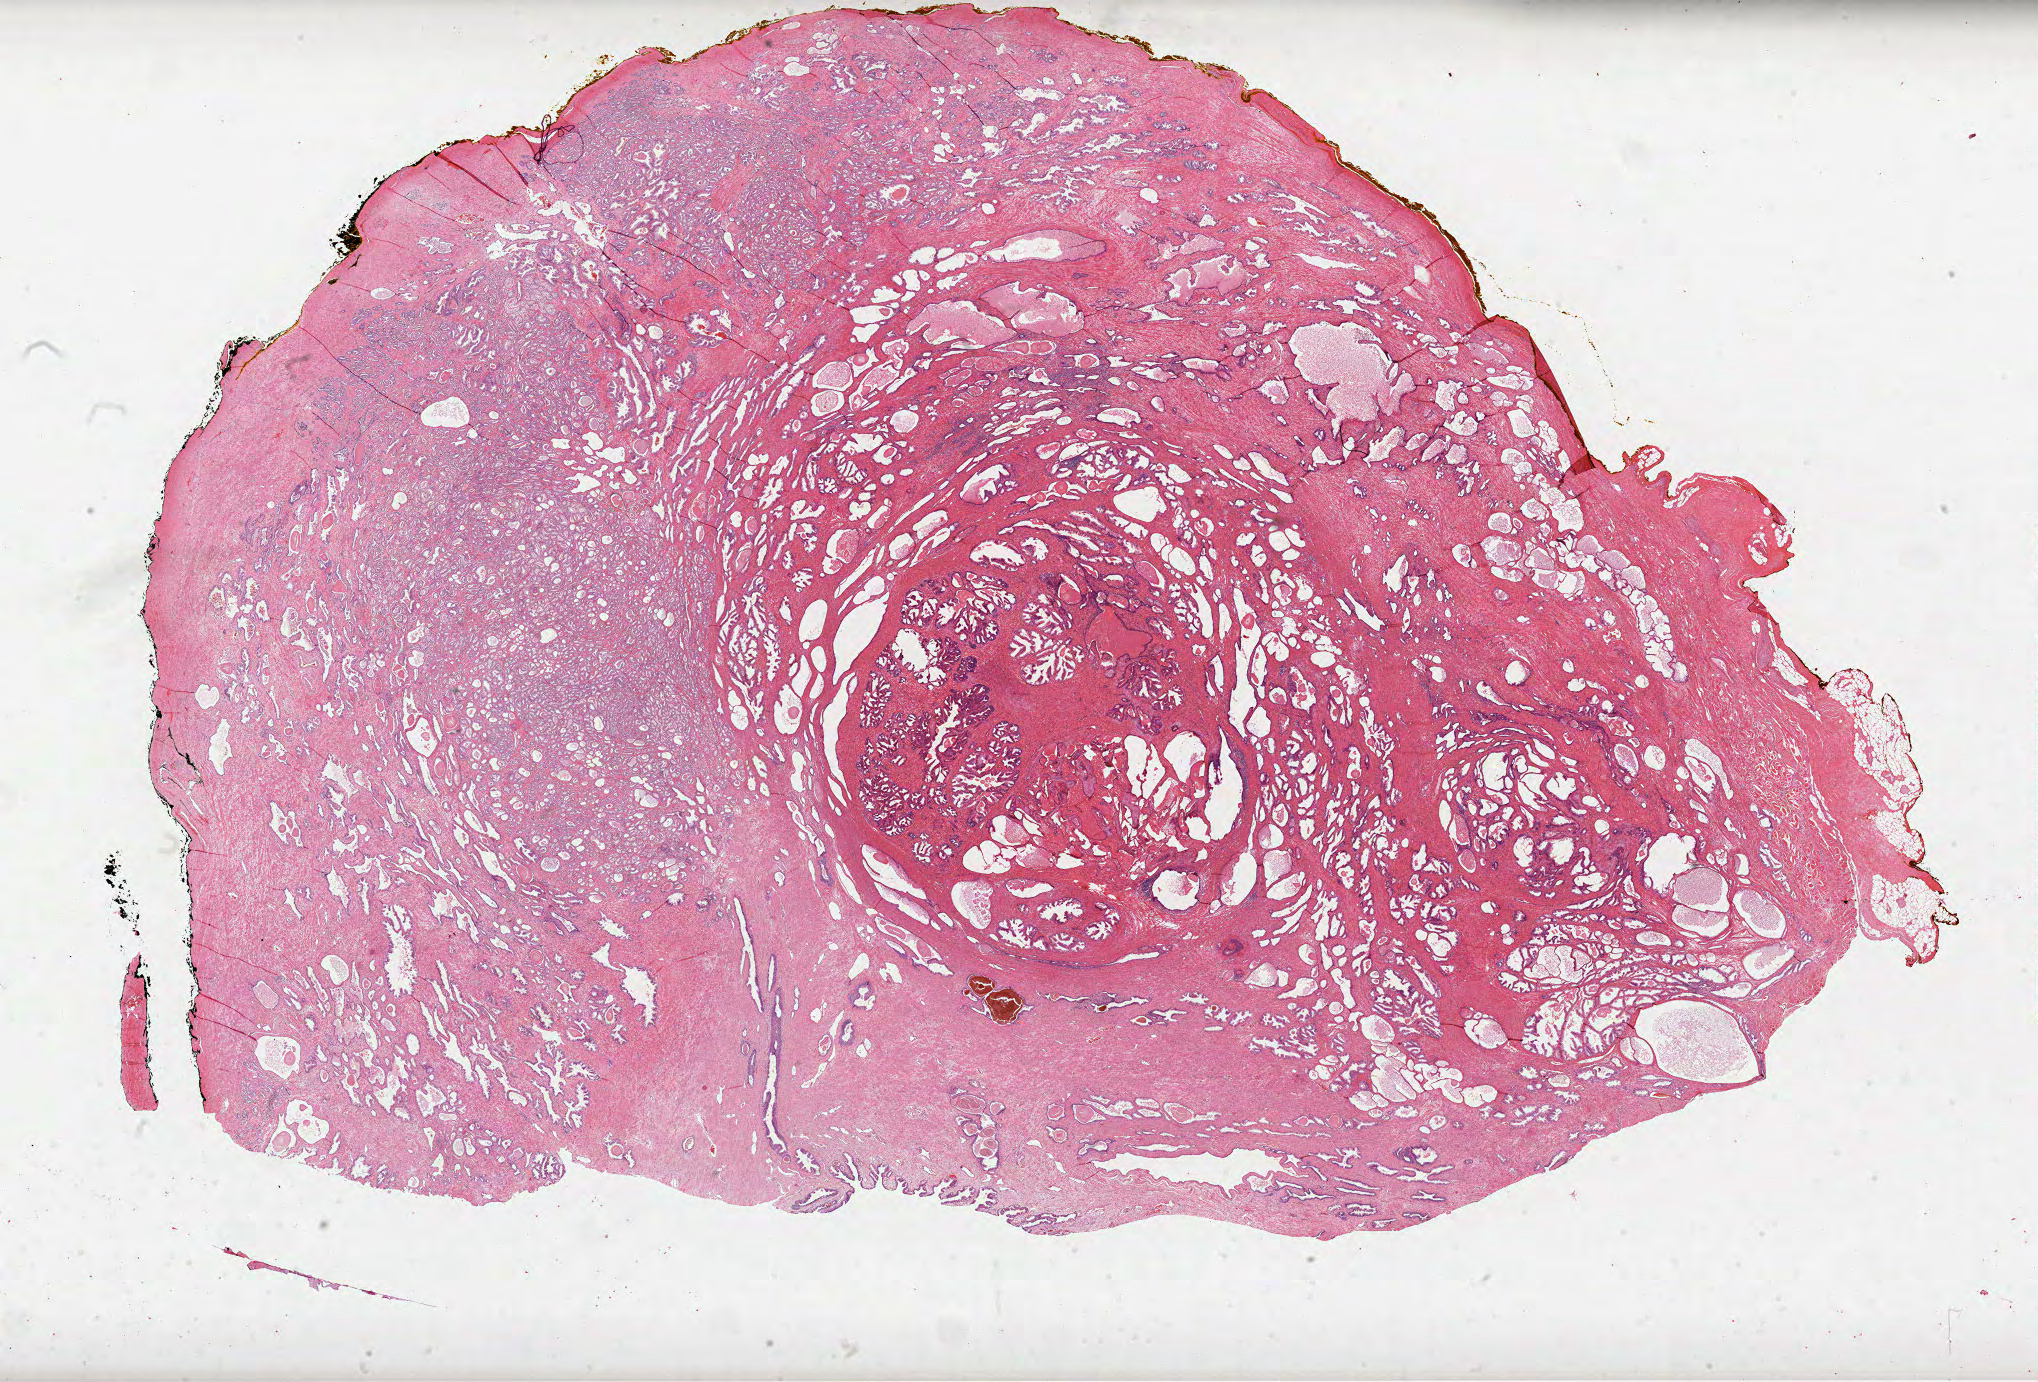
Whole-slide histology image, H&E-stained, whole scanned area (about 32.9 x 22.3 mm) shown as a low-resolution overview; FFPE section; sample: primary tumour, prostate. Male, age 57 years at initial diagnosis. Gleason score: 7 (3+4).
- histologic diagnosis: Acinar cell carcinoma (prostate gland)
- lymph nodes positive (case pathology): 0 of 5 examined
- laterality: bilateral